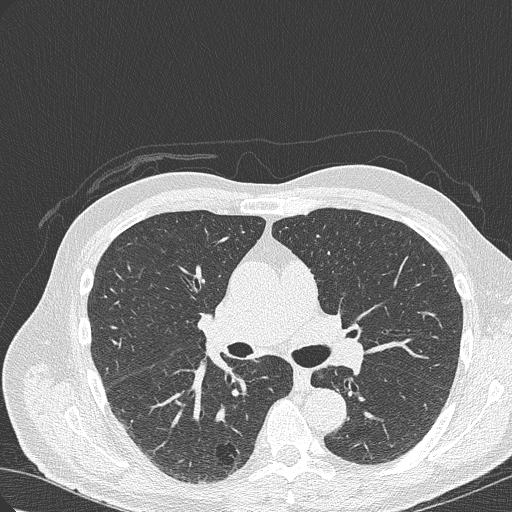
Low-dose screening chest CT, axial slice, baseline screening round, lung window (W 1500 / L -600 HU), lung (sharp) reconstruction kernel (B50f), slice 132 of 322 in the series, 512 × 512 image matrix. Male, age 70 years at enrolment. Current smoker at enrolment.
Lesion marked by an expert reader, bounding box <199,419,263,474> (left, top, right, bottom; pixels). The screening reader recorded 4 non-calcified nodules or masses ≥4 mm on this exam; which of them this box marks is not recorded. Later outcome: lung cancer diagnosed 978 days after this screen — bronchiolo-alveolar adenocarcinoma, NOS, right lower lobe, poorly differentiated (G3), stage IB (AJCC 6th edition), 30 mm at pathology.